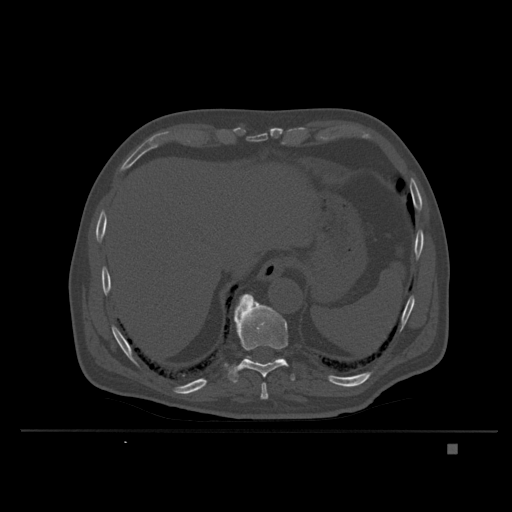
CT including the spine, one axial slice. Slice 194 of 435 in the series (ordered by position). Bone window (W 1800 / L 400 HU). 512 × 512 image matrix. Patient: male, 73 years. From the clinical record (not read from this slice): primary cancer: skin.
Structures marked on this image (semi-automatic segmentation, software-assisted and operator-edited):
- T10 vertebra: bounding box [x1, y1, x2, y2] px = [228, 296, 295, 383]
- T11 vertebra: [234, 294, 283, 362]
- T9 vertebra: [260, 383, 269, 401]